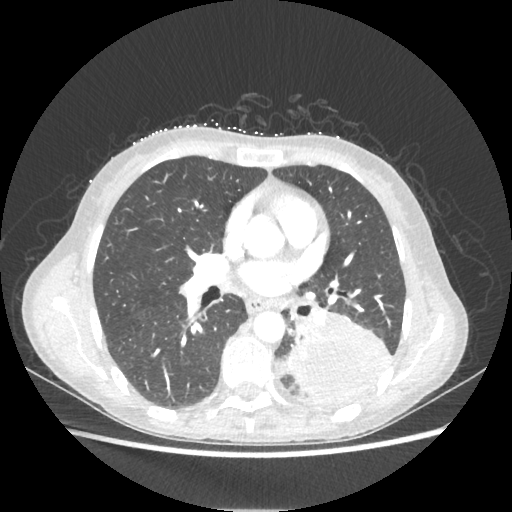
Chest CT, one axial slice; position 115 of 221 along the scan axis; lung window (W 1500 / L -600 HU); 1.25 mm slice thickness; 512 × 512 image matrix, field of view 360 × 360 mm. Female patient, age 53 years. Case-level facts recorded for this patient, not image findings: clinical TNM (as recorded): T3 N0 M0.
Structures marked on this image (bounding box drawn by a radiologist):
- lung tumour (recorded histology: adenocarcinoma): bounding box <286,314,390,401> (left, top, right, bottom; pixels)